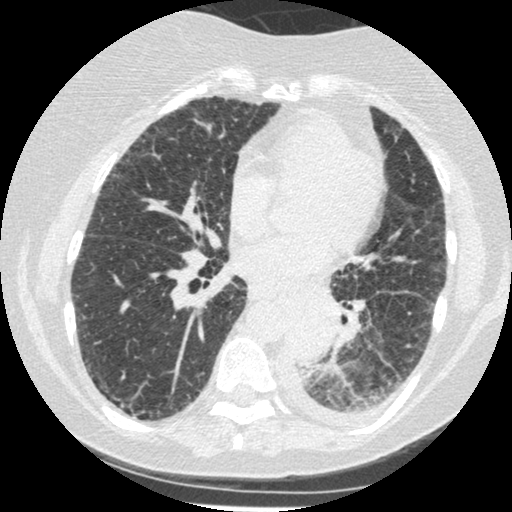
Low-dose screening chest CT, axial slice. Third screening round (two years after baseline). Lung window (W 1500 / L -600 HU). 1.25 mm slice thickness. 120 kVp. Slice 240 of 341 in the series. 512 × 512 image matrix, field of view 310 × 310 mm. Female participant, aged 60 years at enrolment.
- Expert-annotated lung lesion, bounding box (x1, y1, x2, y2) in pixels: (276, 303, 343, 376).
- Screening reader's record for this exam (one nodule recorded; not confirmed to be the boxed lesion): non-calcified nodule or mass ≥4 mm, left lower lobe, 54 × 38 mm, smooth margins, soft tissue attenuation, pre-existing on the prior screen: yes; interval growth: yes.
- Official screen result: positive, other.